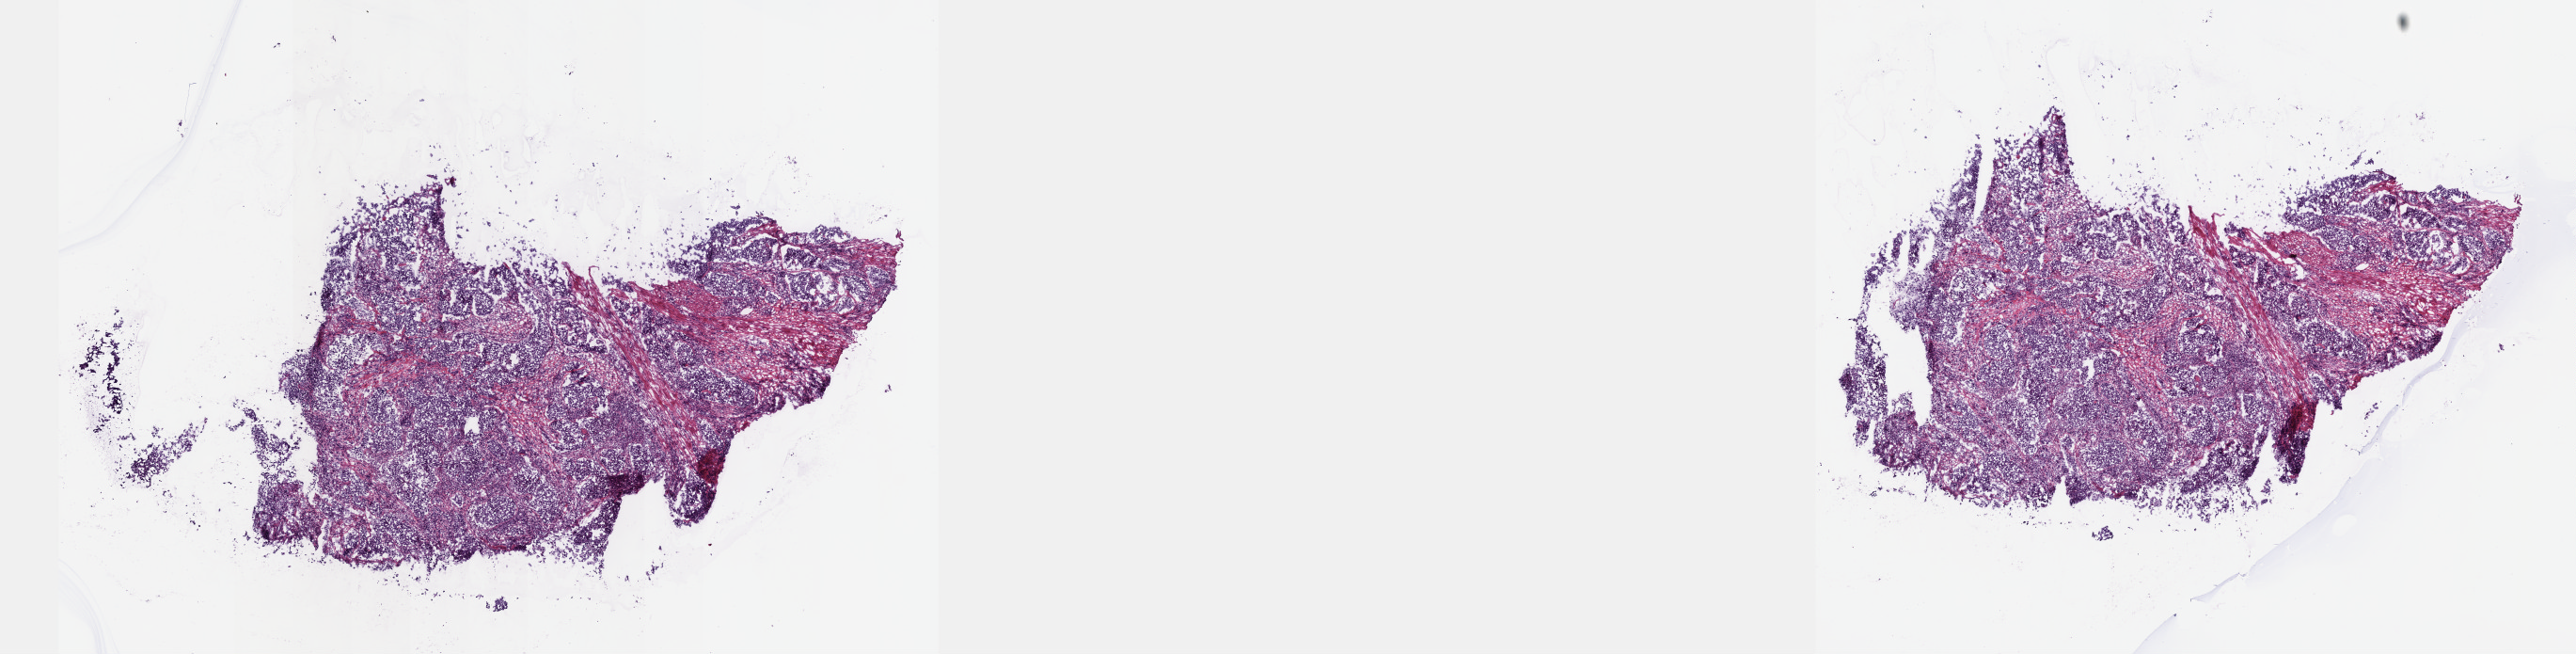
Whole-slide histology image, H&E-stained, a low-resolution overview of the entire scanned area, about 22.1 x 5.6 mm; frozen section from the top of the tissue portion; primary tumour sample from the bladder. Male, age 72 years at initial diagnosis. Histologic grade: high grade. Pathologist review of this section (percent, as recorded): tumour cells 50%, tumour nuclei 90%, normal cells 0%, stromal cells 43%, necrosis 7%. Infiltration values recorded for this section: lymphocyte infiltration 7%, monocyte infiltration 0%, neutrophil infiltration 0%.
AJCC pathologic stage: III (7th edition). Diagnosis: Transitional cell carcinoma. Lymph nodes positive (case pathology): 0 of 5 examined.